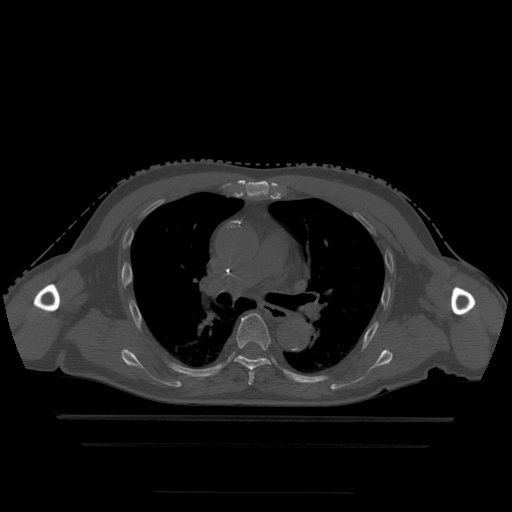
CT including the spine, one axial slice. Bone window (W 1800 / L 400 HU). 512 × 512 image matrix, field of view 436 × 436 mm. Patient age 68 years. From the clinical record (not read from this slice): primary cancer: urothelial.
Outlined on this slice (semi-automatically segmented with operator editing):
- T5 vertebra: bounding box [x1, y1, x2, y2] px = [248, 371, 255, 386]
- T6 vertebra: [235, 314, 271, 372]